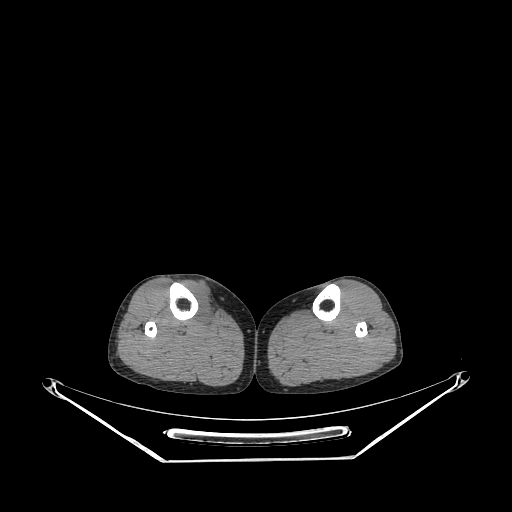
CT of an extremity soft-tissue mass (from a PET/CT study), one axial slice. Slice 141 of 267 in the series (ordered by position). 140 kVp. Soft-tissue window (W 400 / L 40 HU). 512 × 512 image matrix, field of view 500 × 500 mm. Female patient. Case-level facts recorded for this patient, not image findings: histological type: undifferentiated – high grade; grade: high; site of the primary tumour: right thigh.
Structures marked on this image (expert contour drawn on MRI and transferred to this co-registered scan by the dataset authors):
- gross tumour volume (mass): bounding box (x1, y1, x2, y2) in pixels: (181, 281, 213, 316)